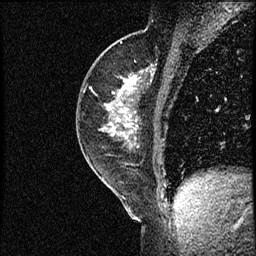
Breast MRI (dynamic contrast-enhanced), one sagittal slice. Slice 31 of 56 in the series (ordered by position). Dynamic contrast-enhanced study with each time point stored as its own series, time point 2 of 3 at this slice position (early post-contrast, ordered by acquisition time). 1.5 T. TE 4.2 ms, TR 17.3 ms. 256 × 256 image matrix, field of view 200 × 200 mm. Female patient. From the clinical record (not read from this slice): setting: breast cancer imaged before/during neoadjuvant chemotherapy; receptor status: HER2-positive.
Annotated regions visible in this slice (semi-automatically segmented with operator editing):
- analysis volume of interest (the breast-tissue region the enhancement analysis was run in; not a lesion): bounding box (x1, y1, x2, y2) in pixels: (76, 50, 156, 155)
- tumour enhancement mask (voxels above the 100 % enhancement threshold inside the analysis volume of interest): (105, 76, 140, 136)